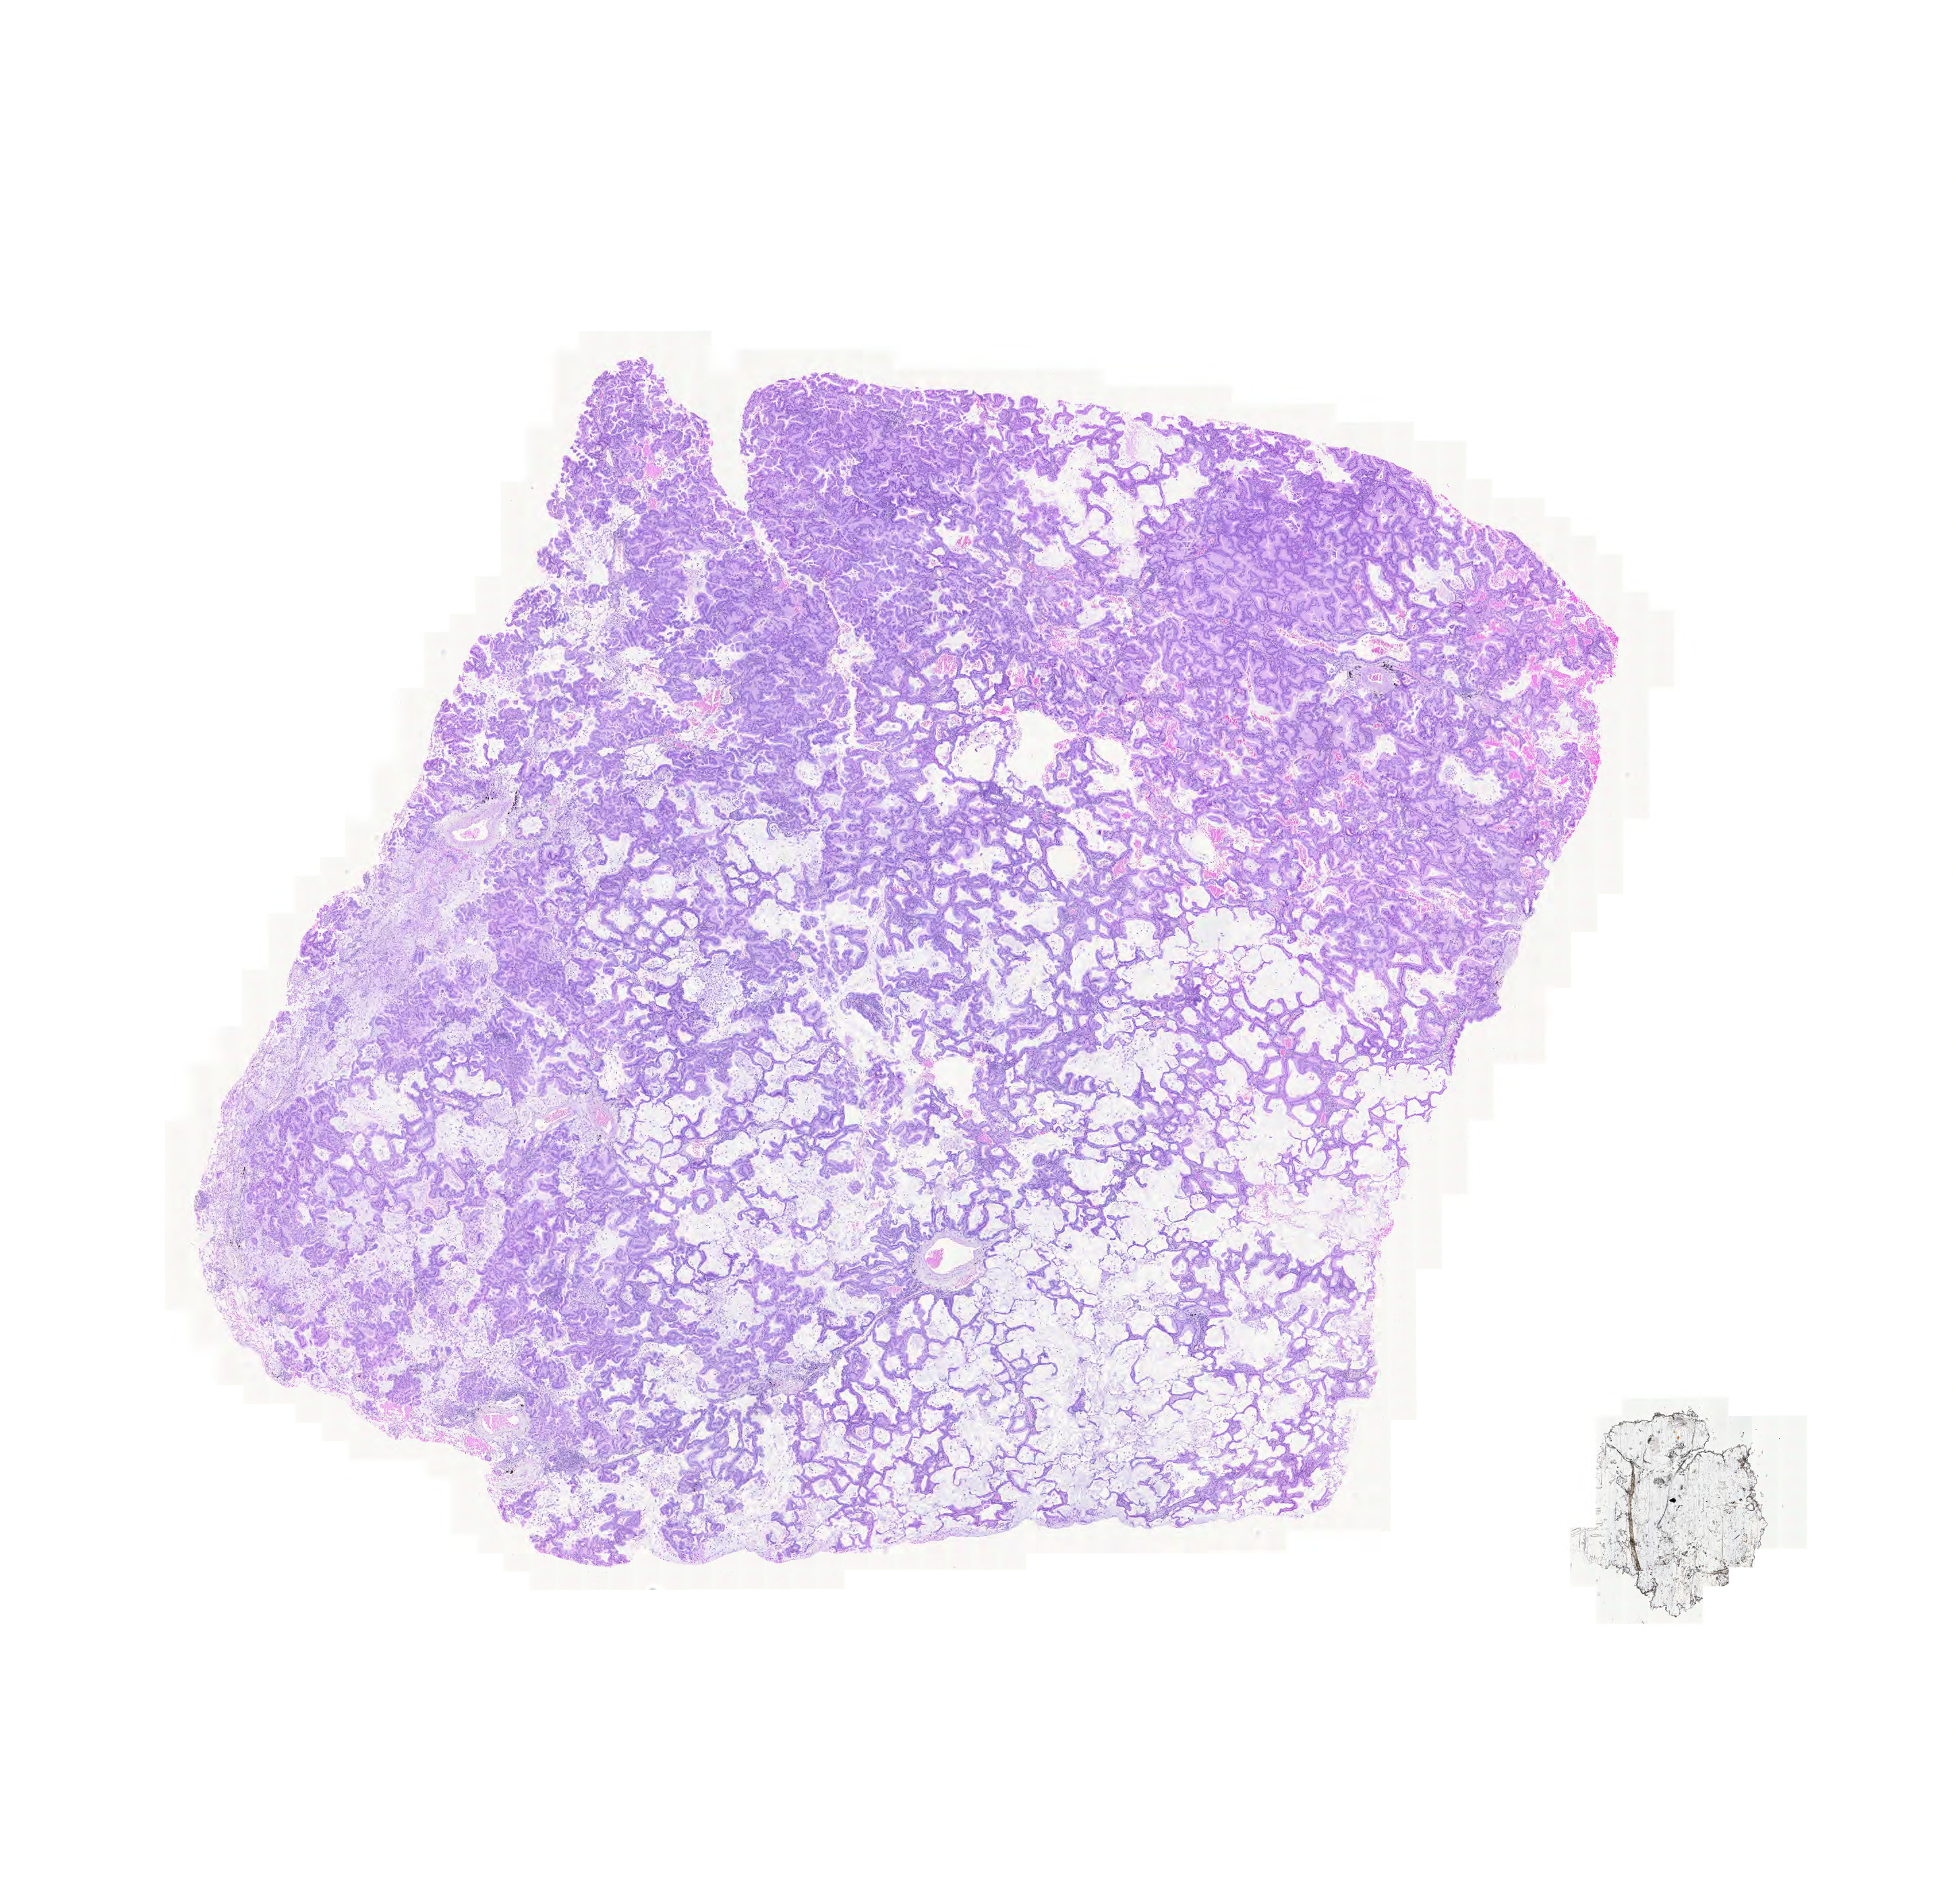
H&E whole-slide image — low-resolution overview of the scanned area, about 21.5 x 21.0 mm, FFPE section, sample: primary tumour, lung. Patient: male, age at initial diagnosis 82 years.
AJCC pathologic stage: IB (6th edition). Laterality: left. Histologic diagnosis: Adenocarcinoma with mixed subtypes (lower lobe, lung).